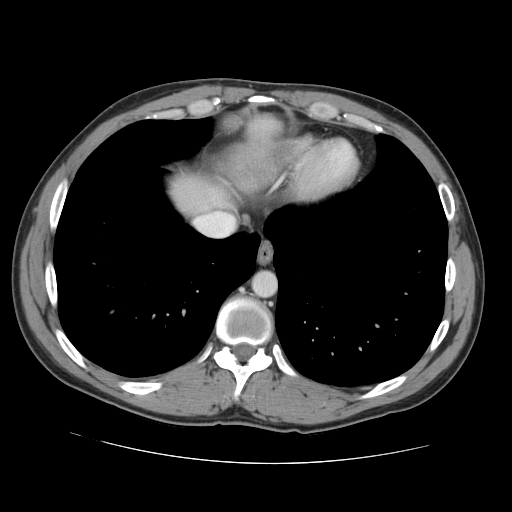
Contrast-enhanced abdominal CT, one axial slice. Position 130 of 131 along the scan axis. 120 kVp. Intravenous contrast given. Soft-tissue window (W 400 / L 40 HU). 2.5 mm slice thickness. 512 × 512 image matrix, field of view 380 × 380 mm. Male patient, age 40 years. From the clinical record (not read from this slice): diagnosis: colorectal cancer liver metastases, imaged before liver resection; multiple liver metastases: yes; largest metastasis: 2.9 cm.
Outlined on this slice (expert manual segmentation):
- hepatic veins: bounding box <195,212,233,236> (left, top, right, bottom; pixels)
- liver: <172,179,227,211>
- planned liver remnant (the part of the liver to remain after resection): <174,179,227,211>